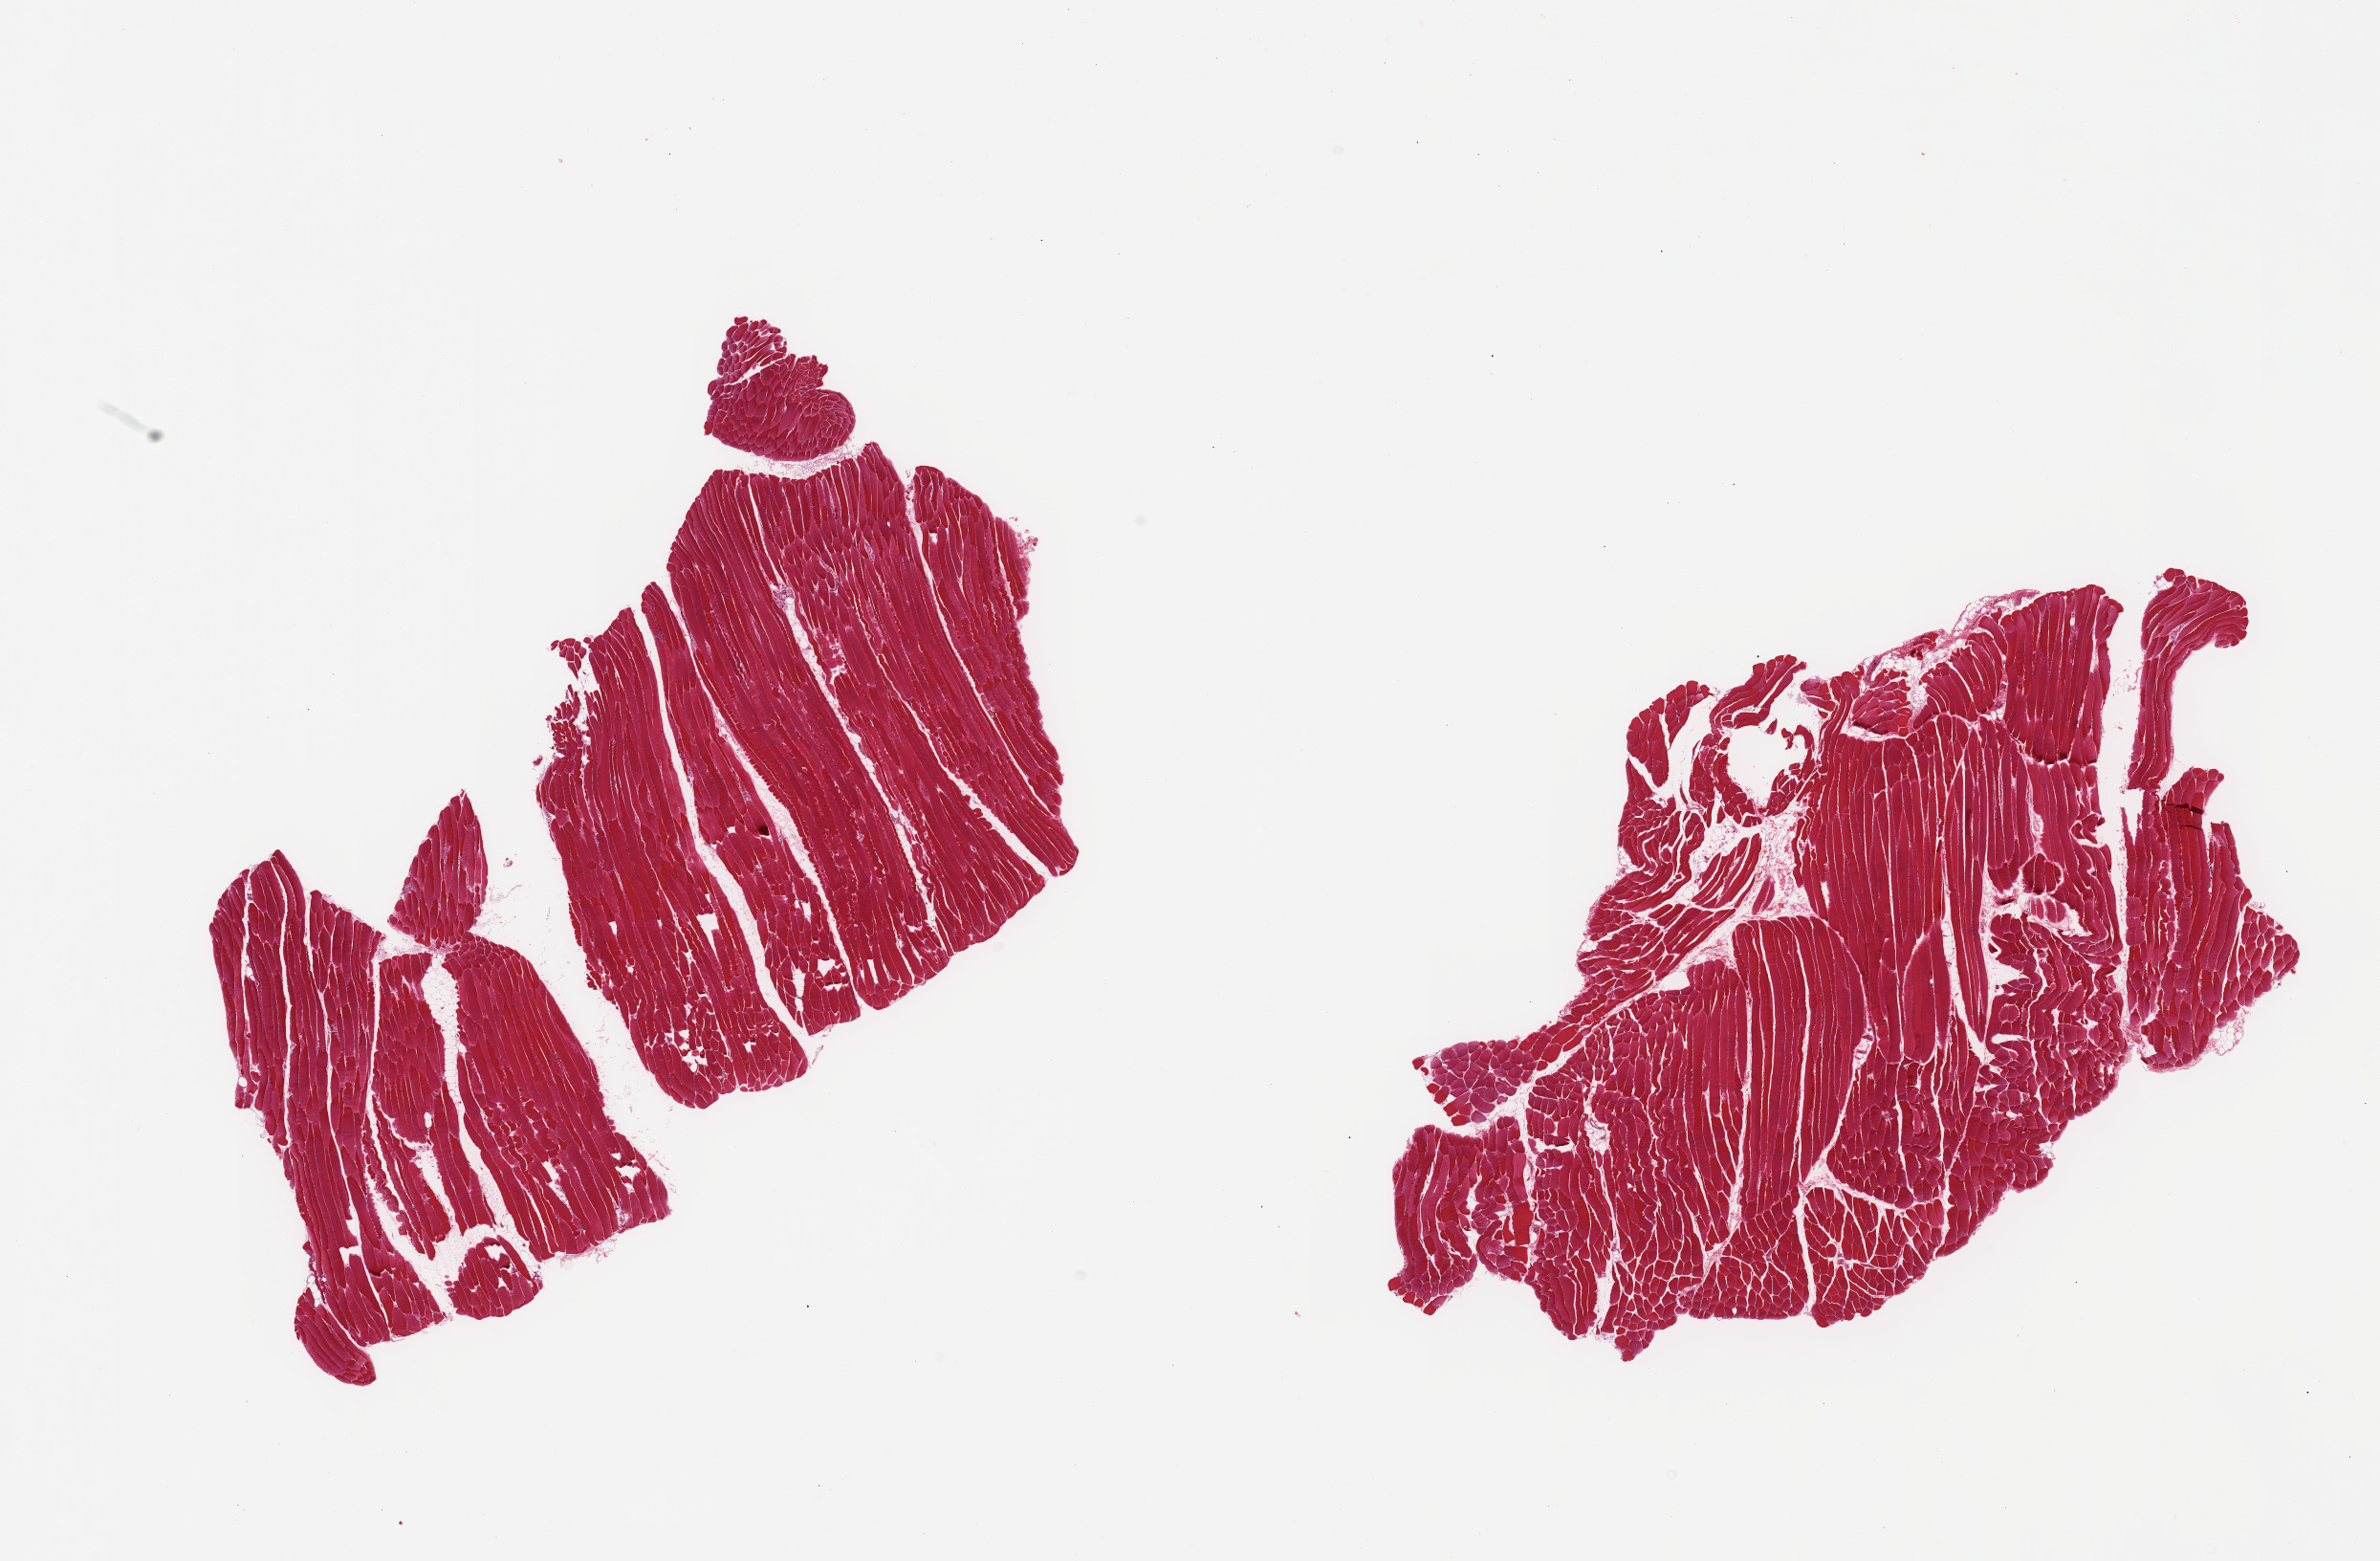
Digitized haematoxylin and eosin-stained section, a low-resolution overview of the entire scanned area, about 19.7 x 12.9 mm; PAXgene-fixed, paraffin-embedded tissue; sampled site (target tissue): skeletal muscle; tissue donor sample. Male donor.
• pathologist's review note for this sample: 2 pieces, trace interstitial fat